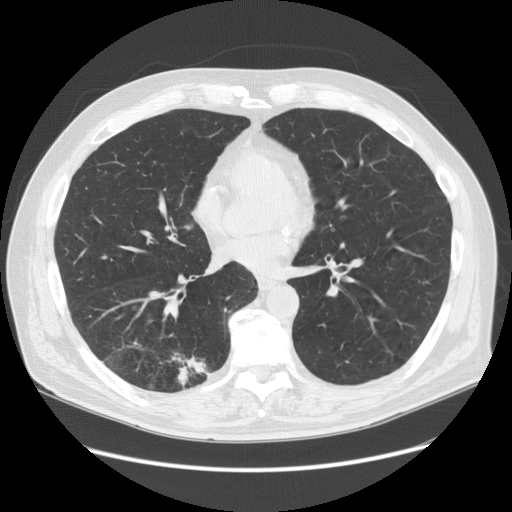
Low-dose screening chest CT, axial slice, baseline annual screen, lung window (W 1500 / L -600 HU), 2.5 mm slice thickness, slice 84 of 149 in the series. Male, age 68 years at enrolment. Former smoker at enrolment.
- Expert-annotated lung lesion, box from (x=122, y=331) to (x=225, y=405) px.
- The exam's reader record, not a measurement of the box and not confirmed to be the same lesion: non-calcified nodule or mass ≥4 mm, right lower lobe, 37 × 20 mm, spiculated (stellate) margins, soft tissue attenuation.
- Official screen result: positive, change unspecified: nodule(s) >= 4 mm or enlarging nodule(s), mass(es), or other non-specific abnormalities suspicious for lung cancer.